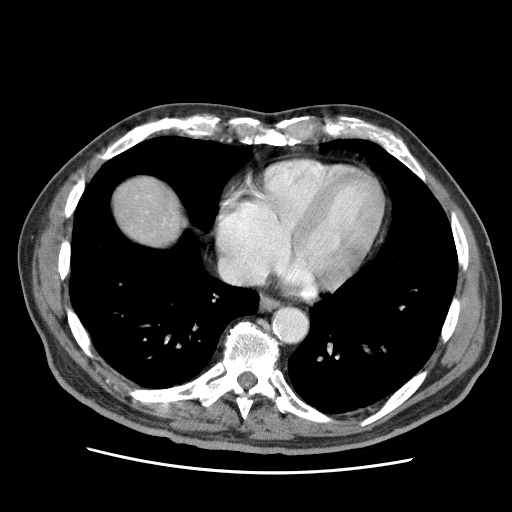
Contrast-enhanced abdominal CT (liver protocol), one axial slice; position 66 of 75 along the scan axis; reconstruction kernel STANDARD; 120 kVp; soft-tissue window (W 400 / L 40 HU); 512 × 512 image matrix, field of view 360 × 360 mm. Case-level facts recorded for this patient, not image findings: diagnosis: hepatocellular carcinoma (patient treated with transarterial chemoembolisation; whether this scan precedes or follows treatment is not stated here); TNM stage (as recorded): Stage-IIIA; Child-Pugh class: A; tumour differentiation: well differentiated; tumour nodularity: multinodular.
Structures marked on this image (semi-automatically segmented with operator editing):
- liver parenchyma outside the tumour (the mass and vessels are separate outlines, so this box may not span the whole liver): bounding box [x1, y1, x2, y2] px = [114, 176, 184, 246]